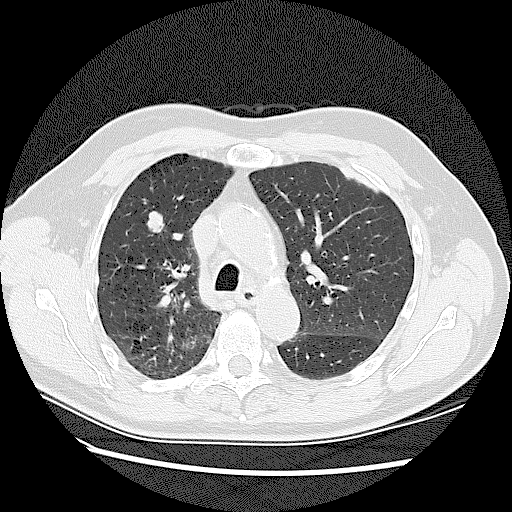
Axial slice from a low-dose chest CT screening exam; first (baseline) screen; lung window (W 1500 / L -600 HU); 2.5 mm slice thickness; lung (sharp) reconstruction kernel (LUNG); 512 × 512 image matrix, field of view 360 × 360 mm. Male participant, aged 72 years at enrolment. Current smoker at enrolment.
Expert reader's lesion annotation, bounding box (x1, y1, x2, y2) in pixels: (133, 204, 182, 242). The screening reader recorded 2 non-calcified nodules or masses ≥4 mm on this exam (right upper lobe, right upper lobe); which of them this box marks is not recorded.